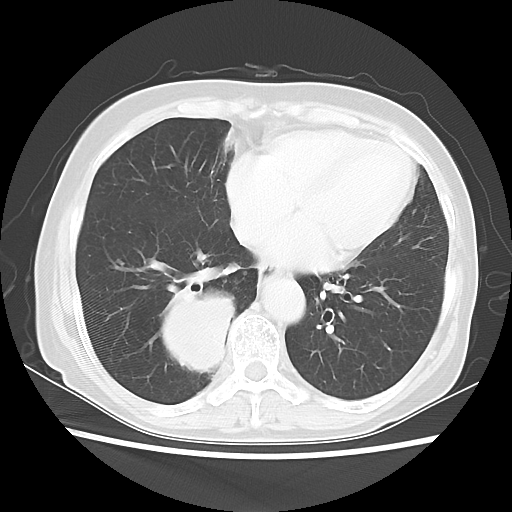
Chest CT, one axial slice. Slice 20 of 56 in the series (ordered by position). 120 kVp. Lung window (W 1500 / L -600 HU). 5 mm slice thickness. 512 × 512 image matrix, field of view 332 × 332 mm. Patient: female, 66 years. Case-level facts recorded for this patient, not image findings: clinical TNM (as recorded): T2 N3 M0; histopathological grade: G3.
Annotated regions visible in this slice (bounding box drawn by a radiologist):
- lung tumour (recorded histology: small cell carcinoma): bounding box <160,283,231,378> (left, top, right, bottom; pixels)